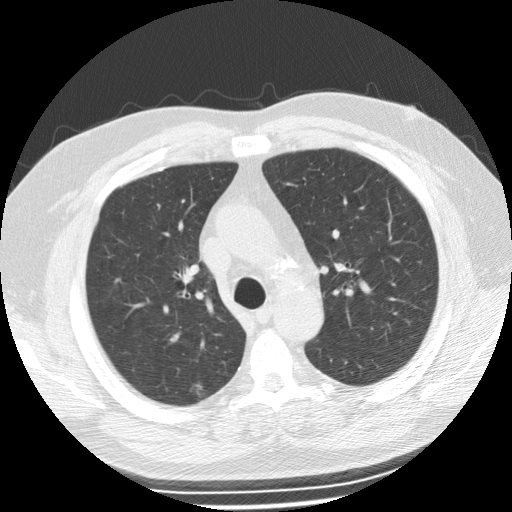
Low-dose screening chest CT, axial slice. Second screening round (one year after baseline). Lung window (W 1500 / L -600 HU). 2.5 mm slice thickness. Standard (soft-tissue) reconstruction kernel (STANDARD). Male, age 62 years at enrolment.
Expert reader's lesion annotation, bounding box [x1, y1, x2, y2] px = [178, 375, 217, 406]. Screening reader's record for this exam (one nodule recorded; not confirmed to be the boxed lesion): non-calcified nodule or mass ≥4 mm, right upper lobe, 6 × 4 mm, poorly defined margins, ground glass attenuation, pre-existing on the prior screen: yes; interval growth: no. Lung cancer was diagnosed 405 days after this screen: bronchiolo-alveolar adenocarcinoma, NOS, right upper lobe, well differentiated (G1), stage IA (AJCC 6th edition), 12 mm at pathology.